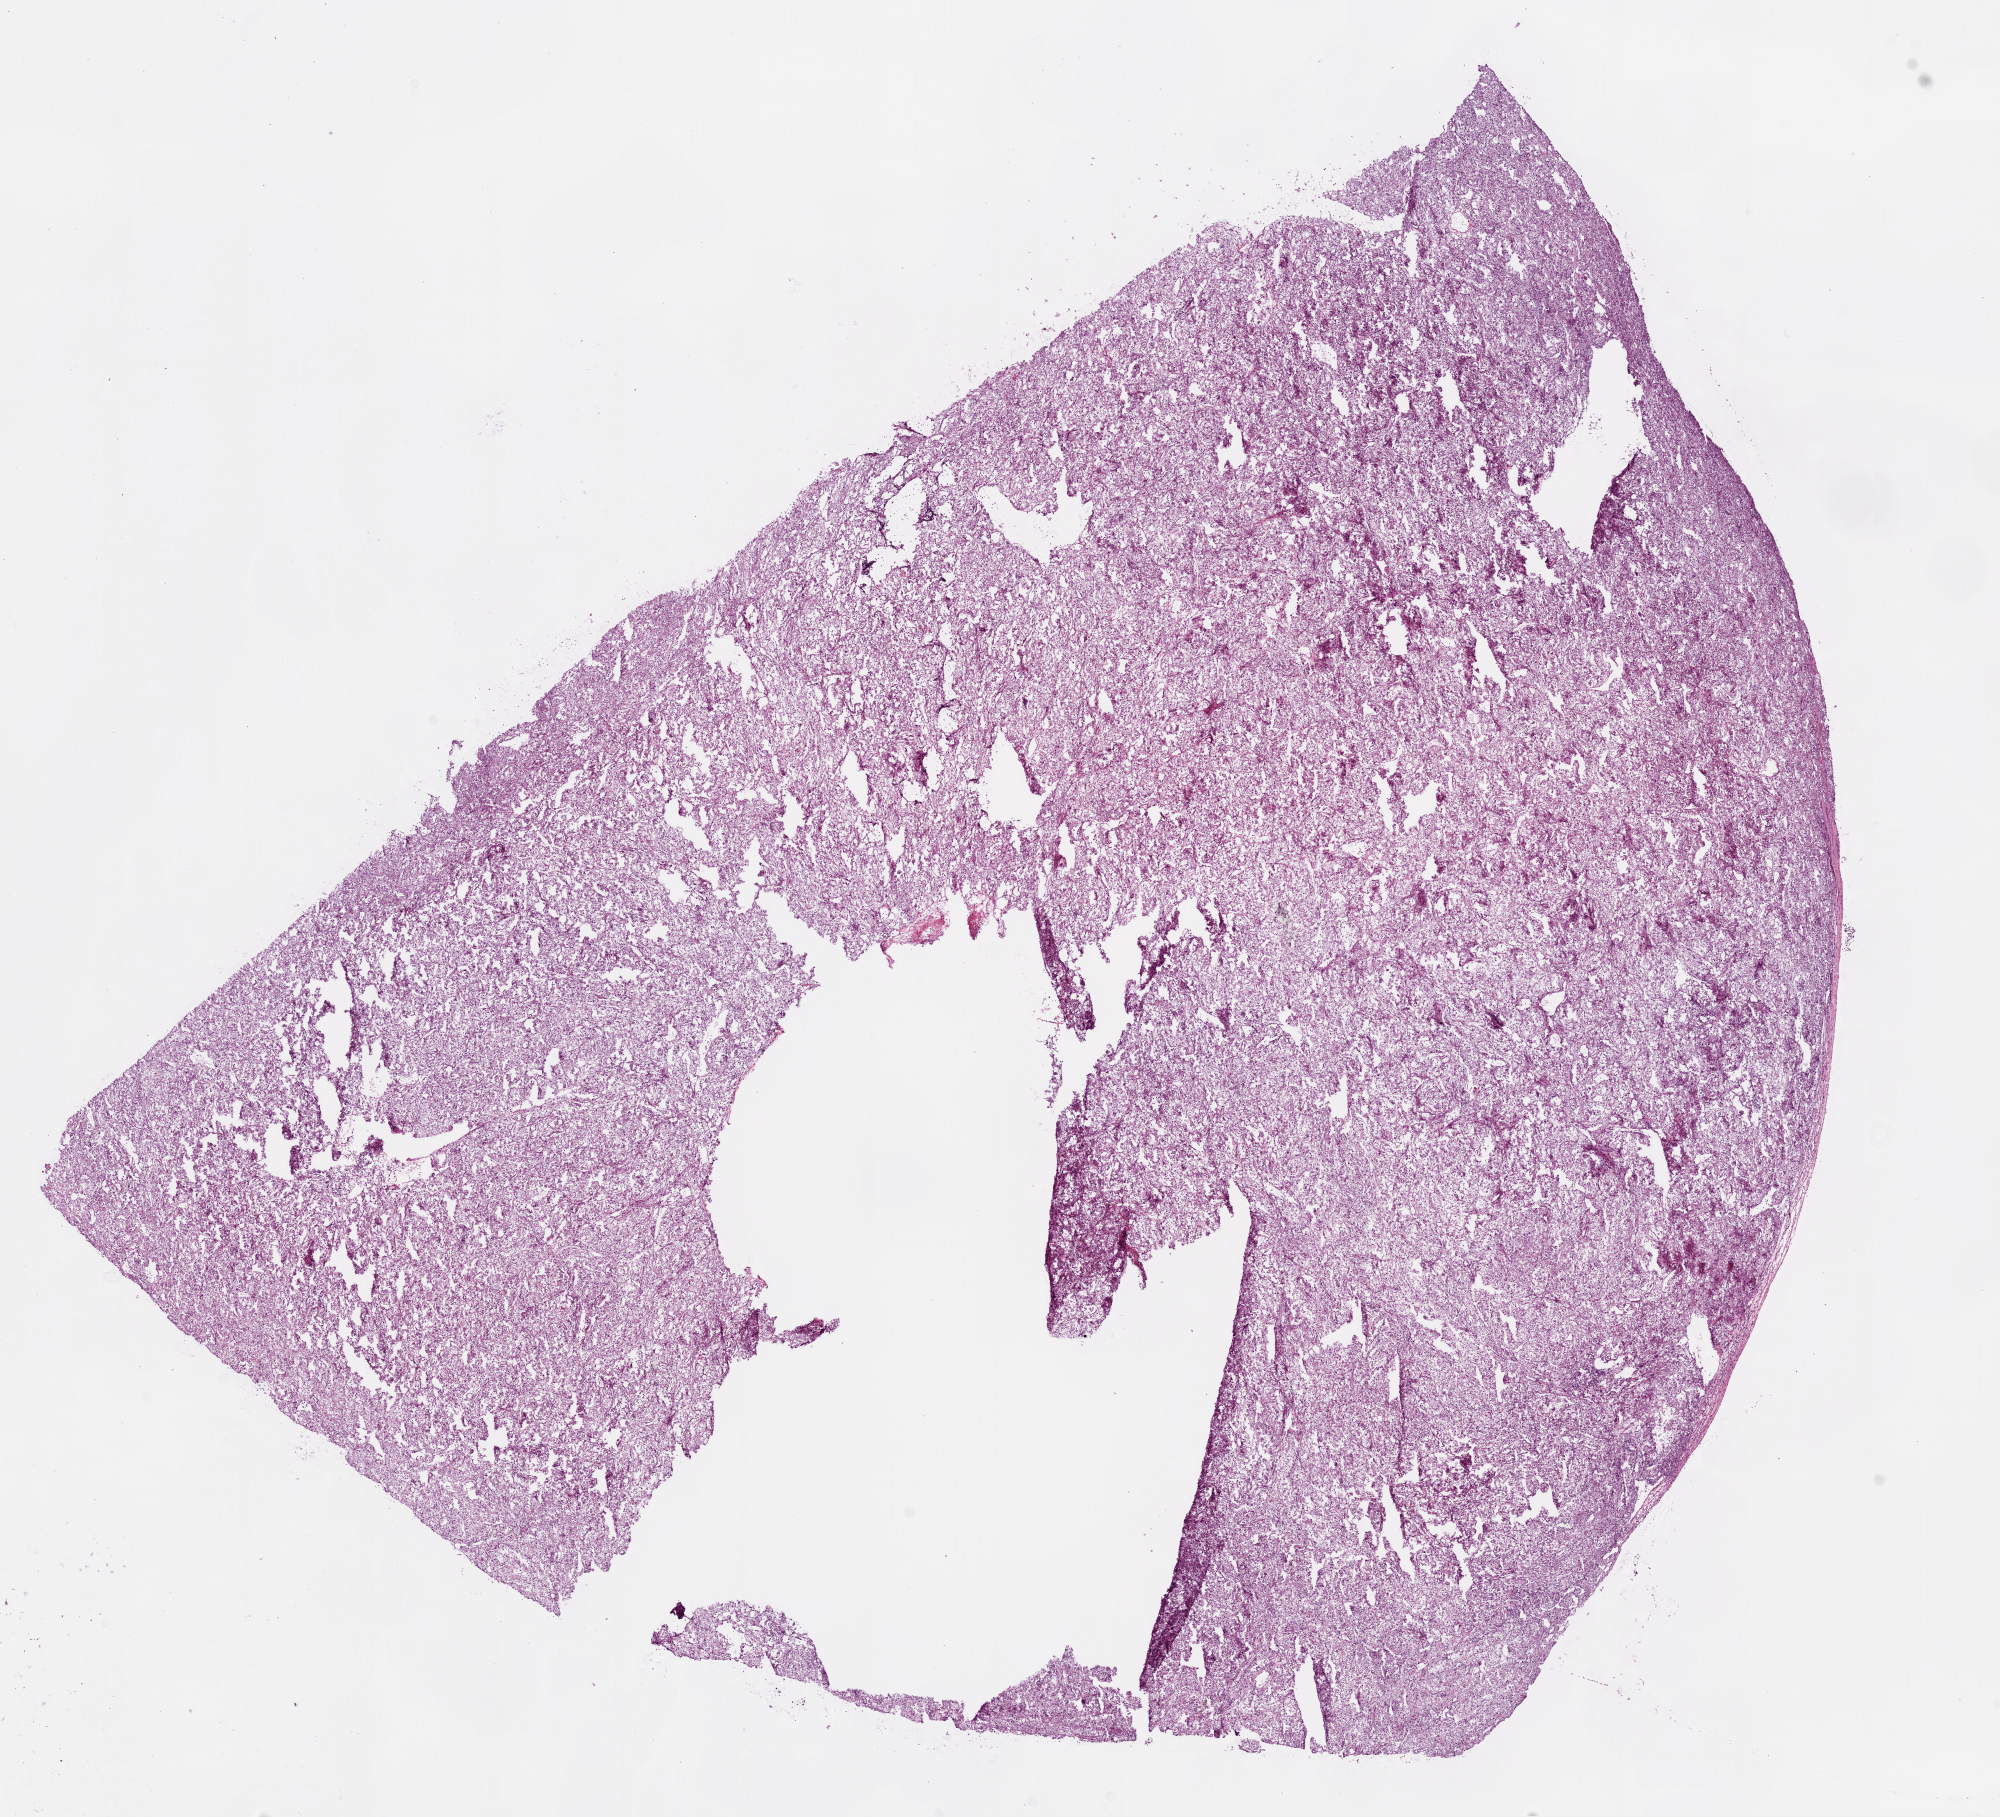
Whole-slide histology image, Hematoxylin and eosin (H&E) stained — low-resolution overview of the scanned area, about 16.0 x 14.6 mm. Frozen section. Sample: primary tumour, kidney. Male patient; age at initial diagnosis 65 years.
Pathologic diagnosis: Clear cell adenocarcinoma, NOS.